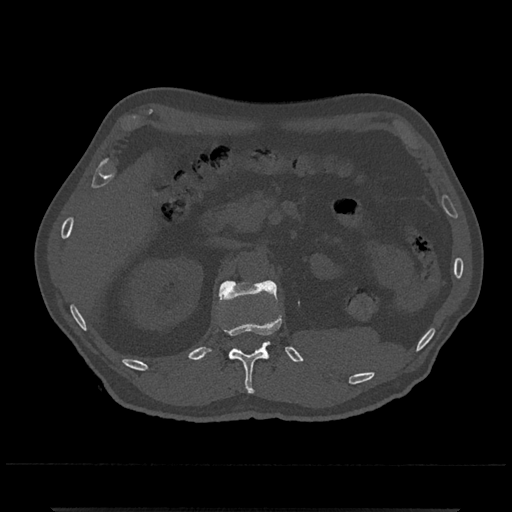
CT including the spine, one axial slice; slice 408 of 797 in the series (ordered by position); reconstruction kernel Br40s/3; bone window (W 1800 / L 400 HU); 0.5 mm slice thickness; 512 × 512 image matrix. Patient: male, 67 years. Case-level facts recorded for this patient, not image findings: primary cancer: prostate.
Outlined on this slice (semi-automatic segmentation, software-assisted and operator-edited):
- L1 vertebra: bounding box <219,280,278,358> (left, top, right, bottom; pixels)
- T12 vertebra: <226,317,282,394>